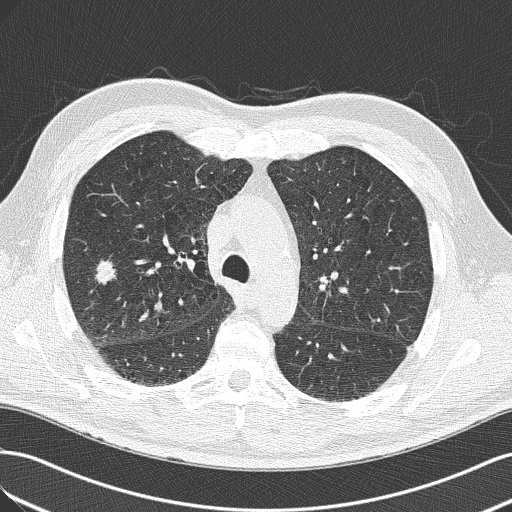
Low-dose screening chest CT, one axial slice; slice 92 of 143 in the series (ordered by position); lung window (W 1500 / L -600 HU); 512 × 512 image matrix.
Outlined on this slice (expert manual segmentation):
- lesion 1 (tumor, lower lobe of right lung): box from (x=95, y=260) to (x=116, y=285) px